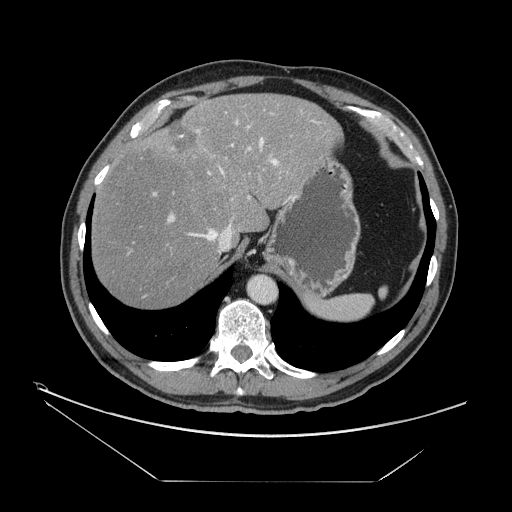
Contrast-enhanced abdominal CT, one axial slice. Position 120 of 161 along the scan axis. 120 kVp. Soft-tissue window (W 400 / L 40 HU). 2.5 mm slice thickness. 512 × 512 image matrix. Male patient, age 65 years. From the clinical record (not read from this slice): diagnosis: colorectal cancer liver metastases, imaged before liver resection; multiple liver metastases: yes; largest metastasis: 4.2 cm; disease in both lobes: yes.
Outlined on this slice (manually delineated by an expert):
- hepatic veins: bounding box <187,138,263,253> (left, top, right, bottom; pixels)
- liver: <91,93,339,311>
- planned liver remnant (the part of the liver to remain after resection): <91,94,339,311>
- portal vein (with intrahepatic branches): <153,109,303,223>
- liver metastasis: <167,121,197,154>